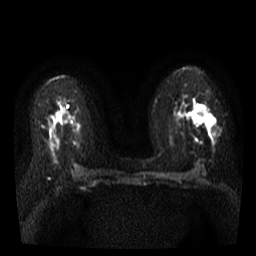
Breast MRI, one axial slice. Slice 18 of 35 in the series (ordered by position). Diffusion-weighted series; image 2 of 4 stored at this slice position (different b-values; order by instance number). 3 T. 5 mm slice thickness. 256 × 256 image matrix. Female patient.
Annotated regions visible in this slice (expert manual segmentation):
- tumour on diffusion-weighted imaging: bounding box (x1, y1, x2, y2) in pixels: (195, 108, 216, 125)